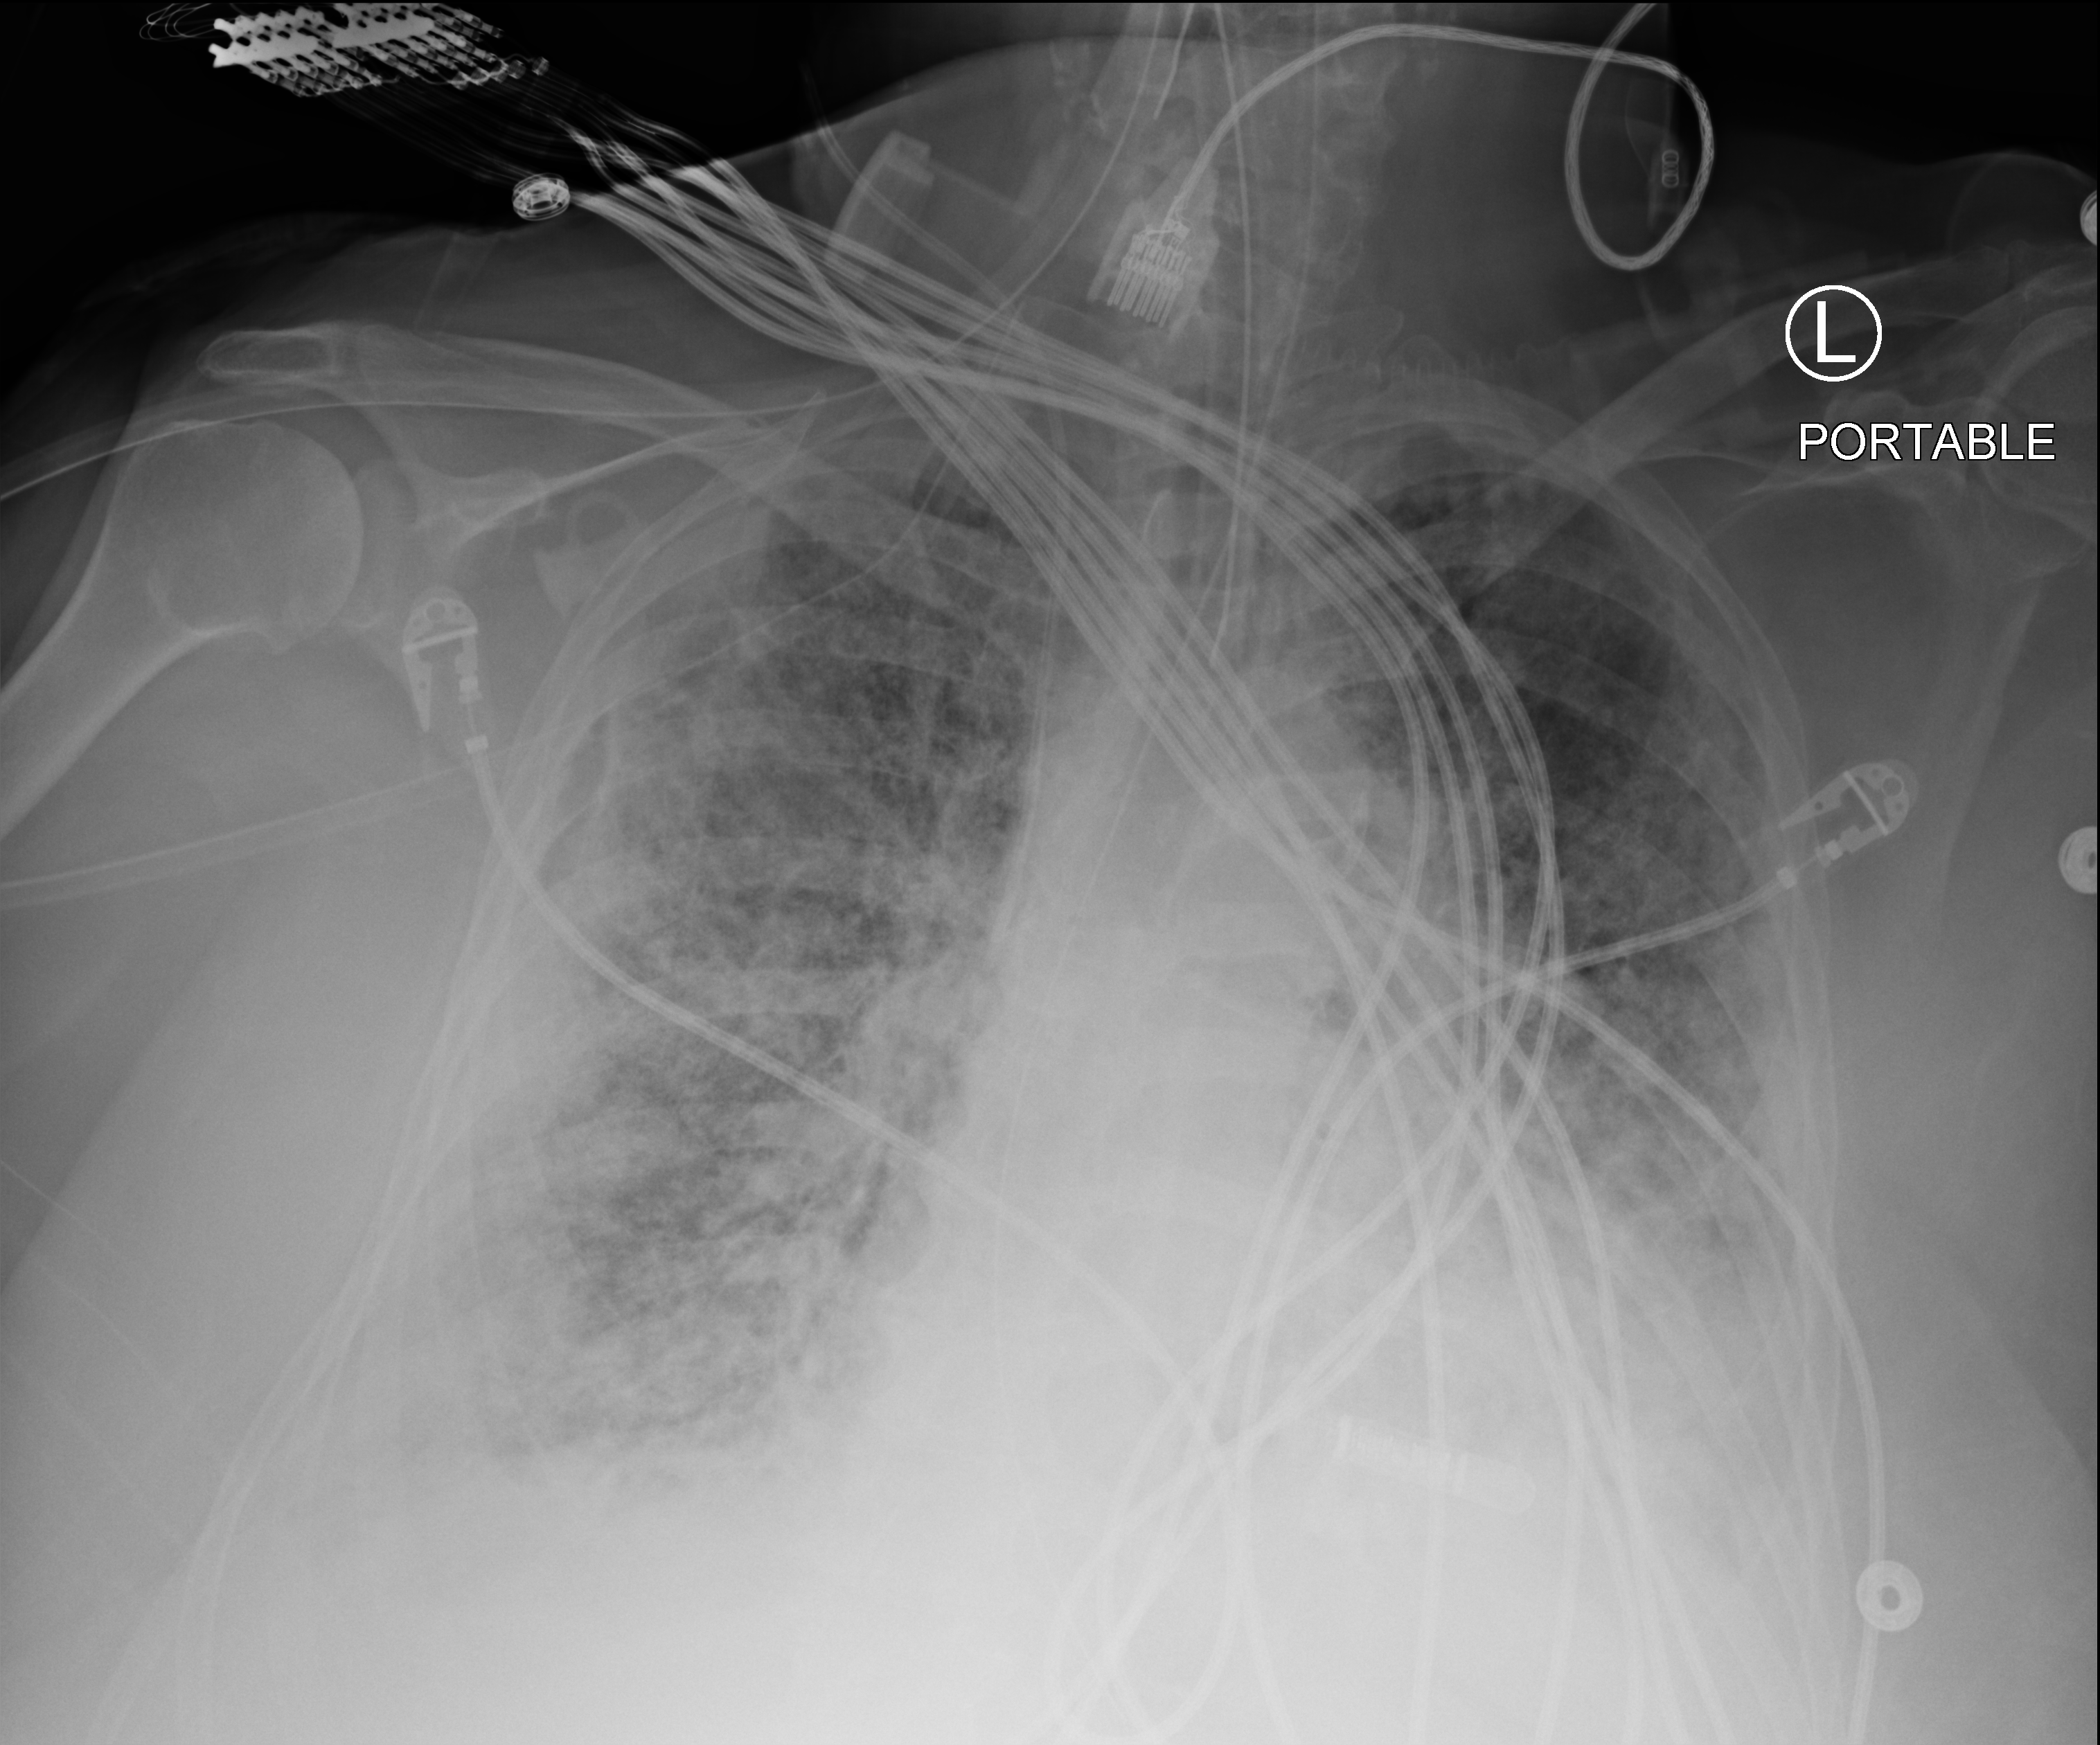
Chest X-ray (portable), anteroposterior (AP) projection. Patient hospitalised with COVID-19; female, aged 60–74 years.
Admission-level facts for this patient (not findings on this image; timing relative to this image not recorded):
- COPD (admission record): no
- smoking status (admission record): former
- admitted to intensive care during this hospital stay: yes